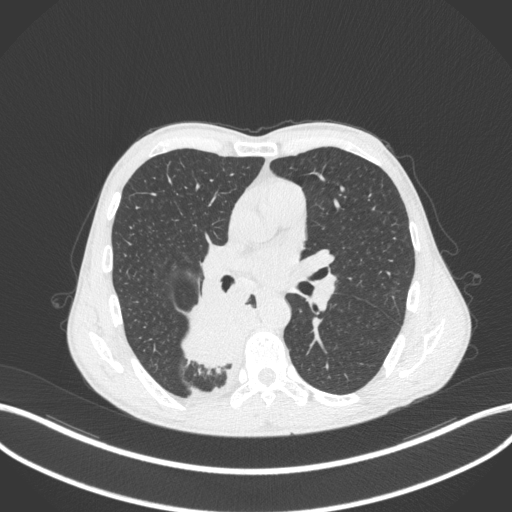
Chest CT, one axial slice; slice 206 of 371 in the series (ordered by position); 120 kVp; lung window (W 1500 / L -600 HU); 1 mm slice thickness; 512 × 512 image matrix, field of view 400 × 400 mm. Patient: male, 58 years. From the clinical record (not read from this slice): clinical TNM (as recorded): T3 N1 M1.
Annotated regions visible in this slice (bounding box drawn by a radiologist):
- lung tumour (recorded histology: squamous cell carcinoma): bounding box <176,295,251,372> (left, top, right, bottom; pixels)